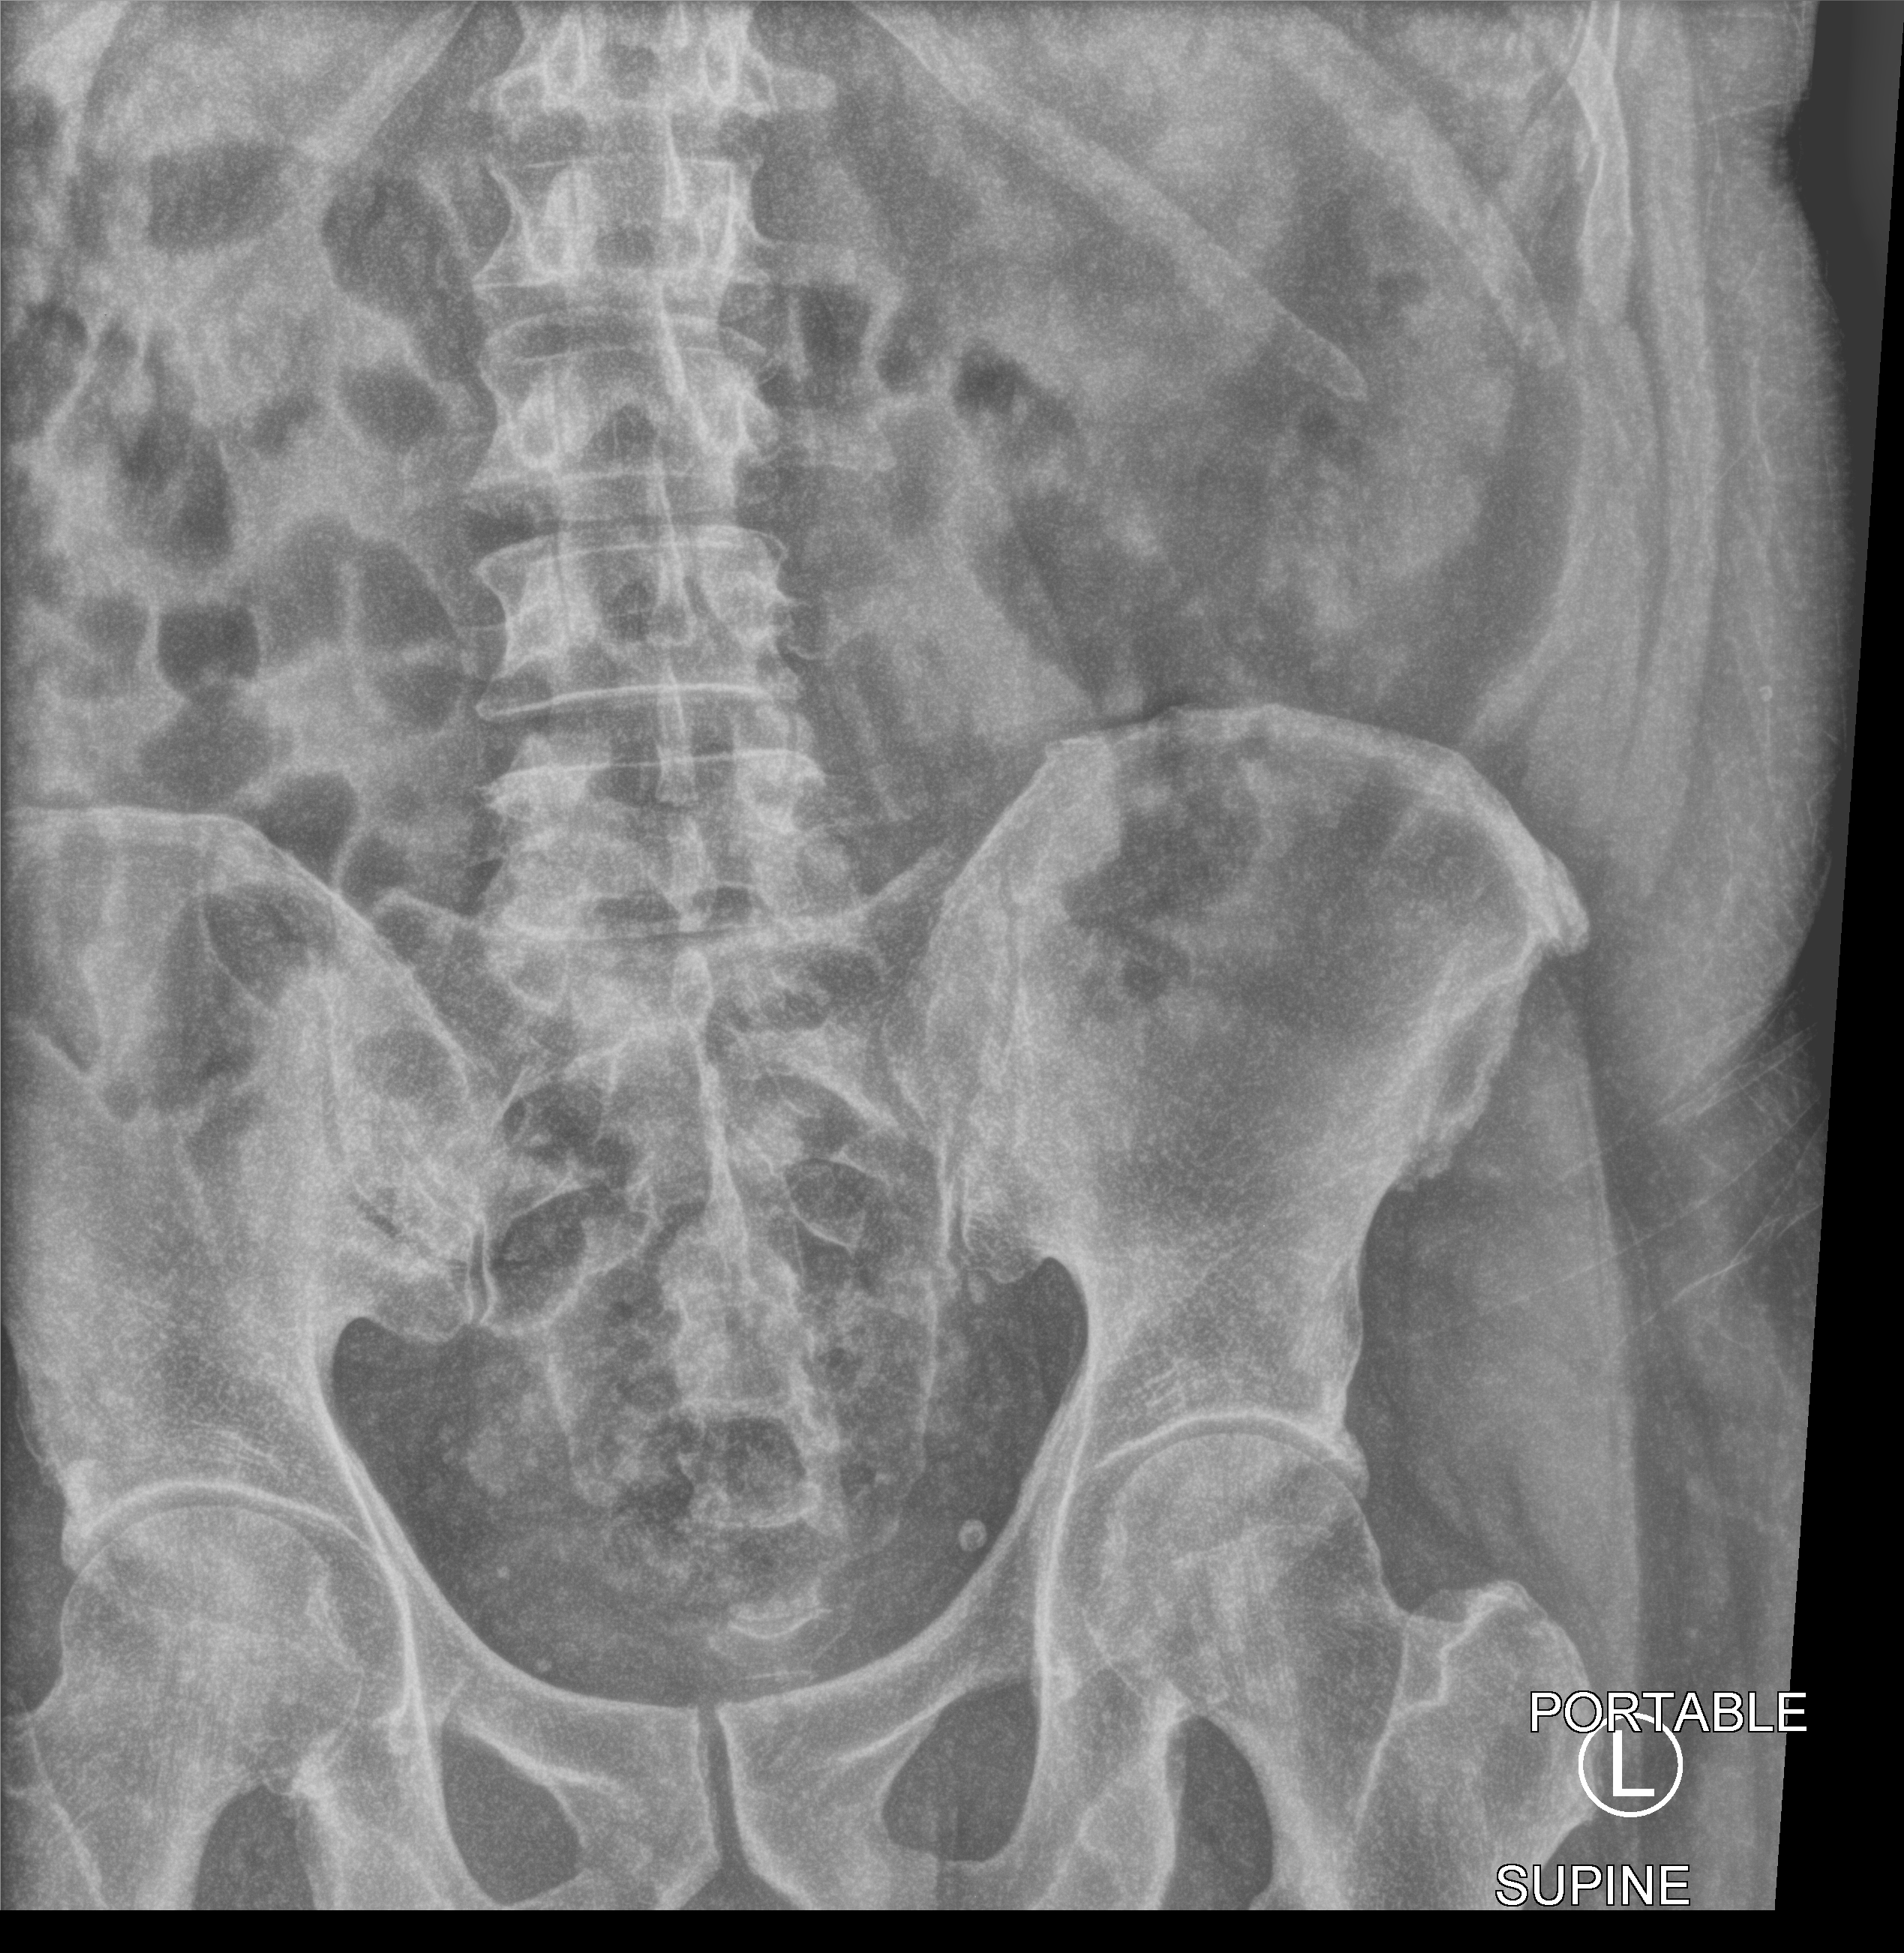
Bedside abdomen radiograph (computed radiography), anteroposterior (AP) projection. Patient hospitalised with COVID-19; male, aged 18–59 years.
From the hospital-stay record, not from the radiograph (when in the stay this image was taken is not recorded):
- mechanically ventilated during this hospital stay: no
- COPD (admission record): no